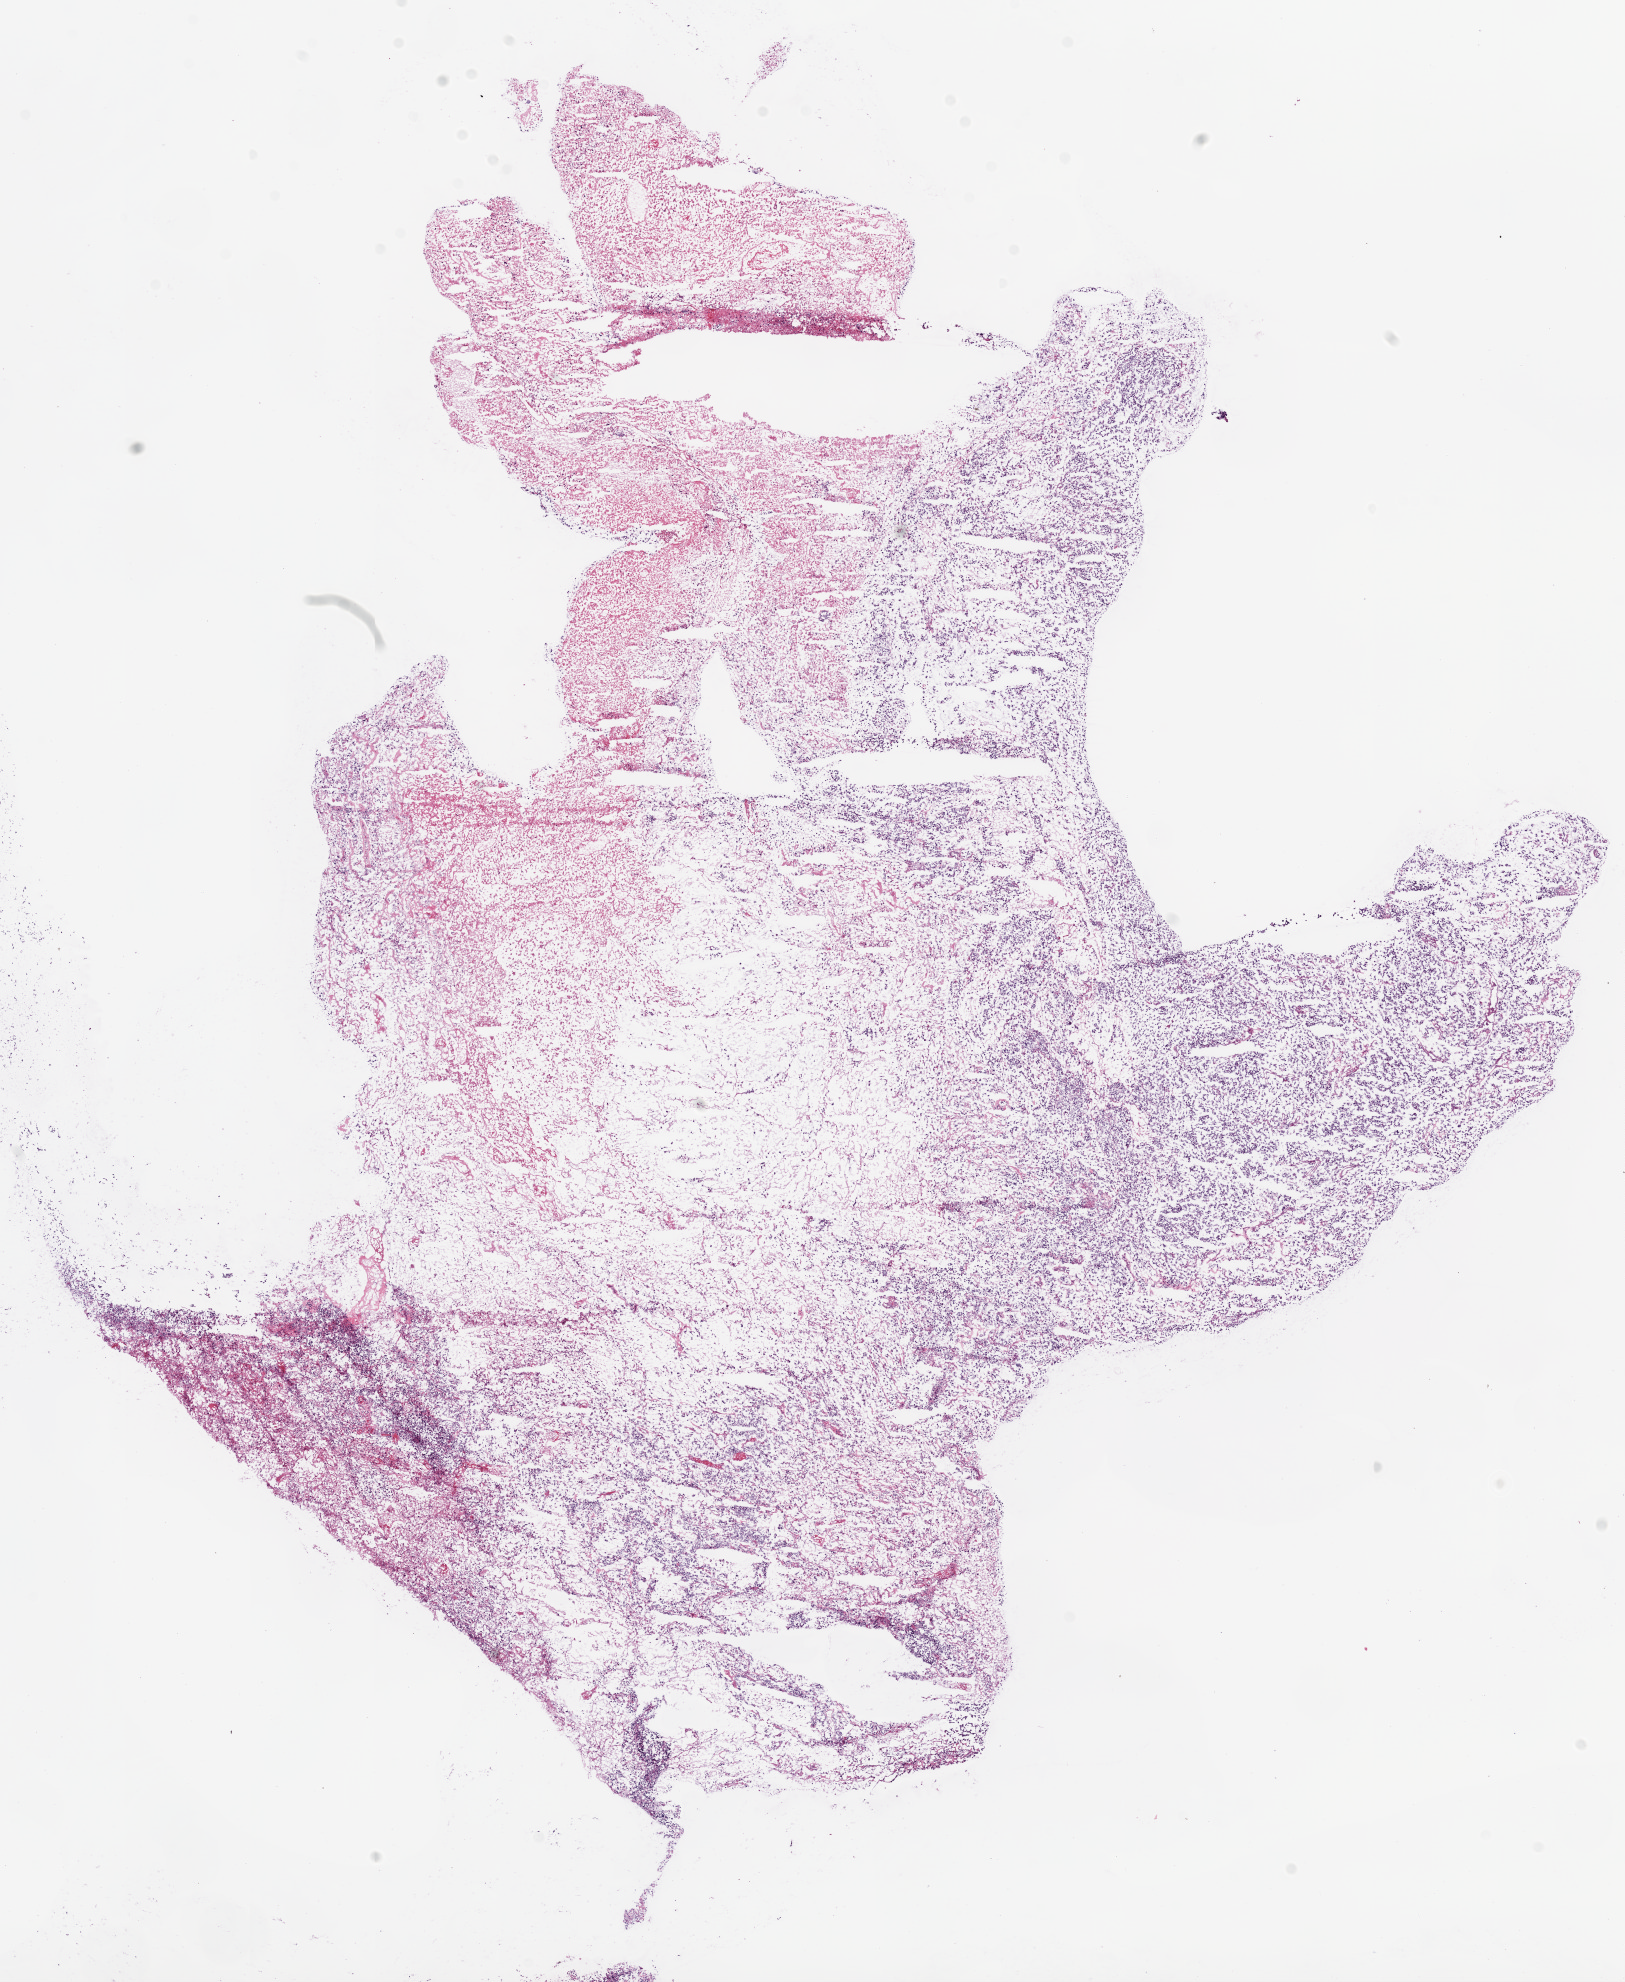
Whole-slide histology image, H&E — shown as a low-resolution overview of the whole scanned area (about 13.0 x 15.9 mm, from a 20x scan); frozen section from the top of the tissue portion; sample: primary tumour, brain. Male patient; age at initial diagnosis 43 years. Slide review estimates, as recorded: tumour cells 85%, tumour nuclei 80%.
Diagnosis: Glioblastoma.